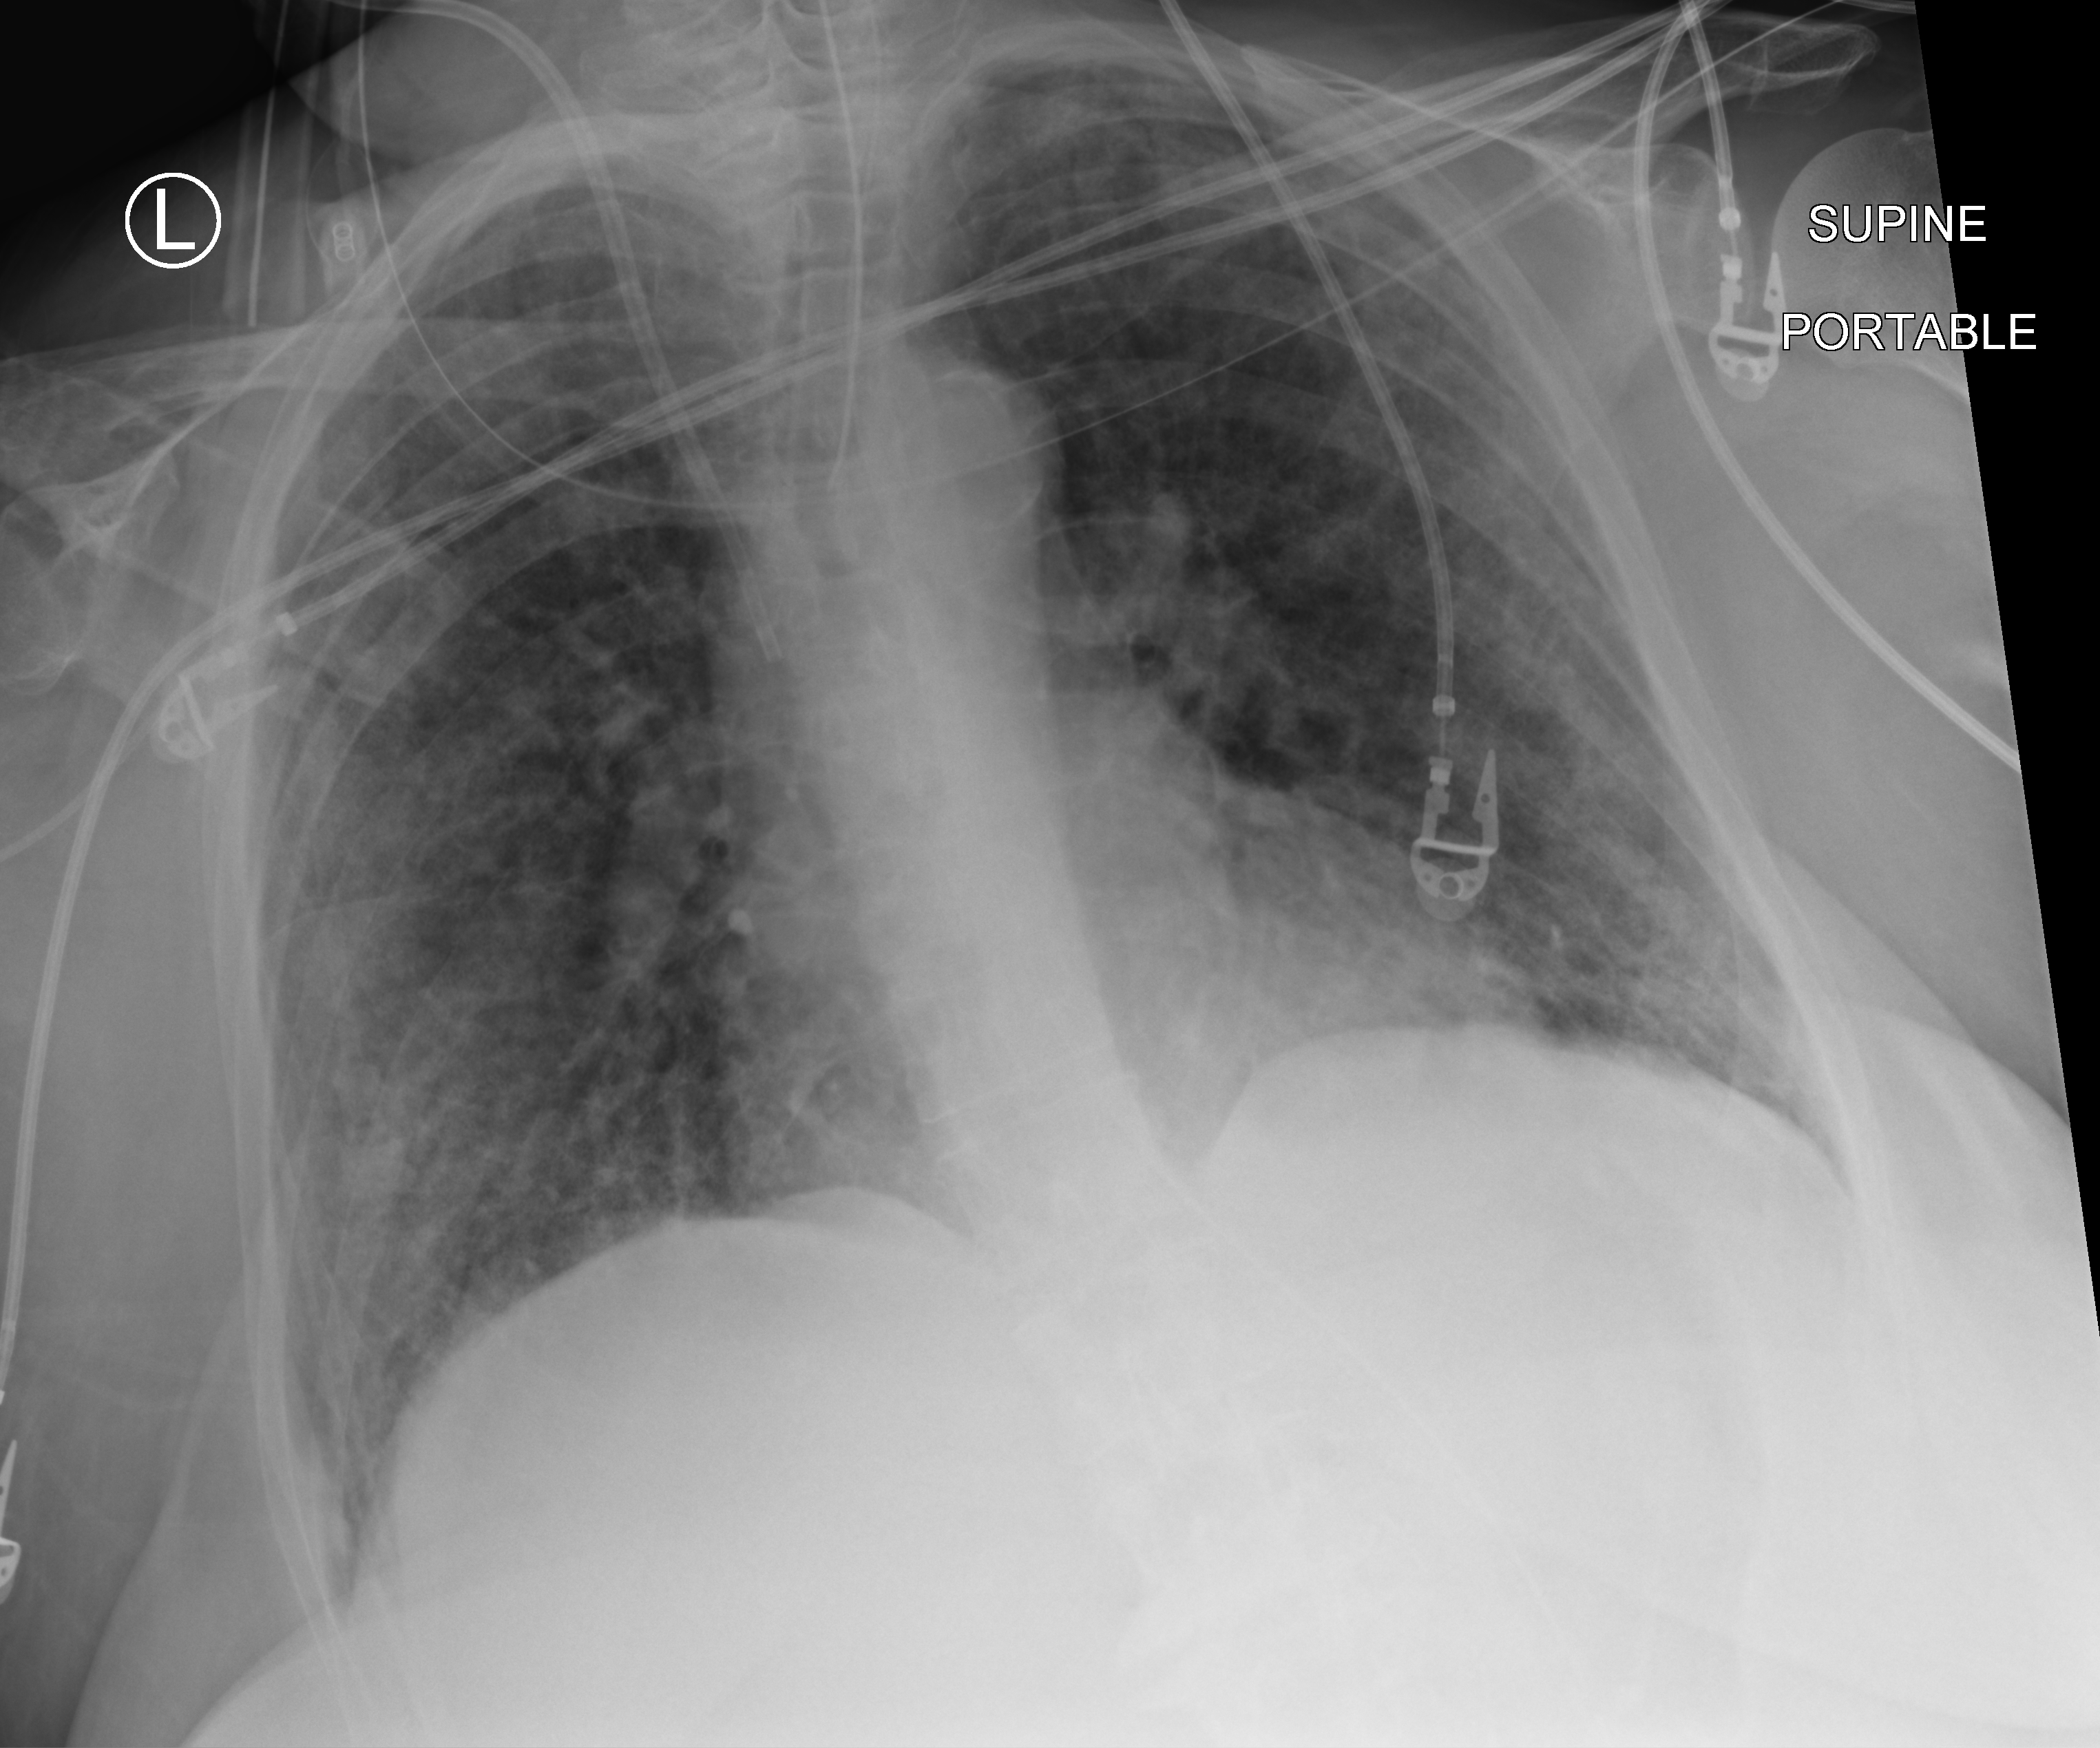
Bedside chest radiograph (computed radiography). Female patient hospitalised with COVID-19, age 75–90 years.
Admission-level facts for this patient (not findings on this image; timing relative to this image not recorded):
- admitted to intensive care during this hospital stay: yes